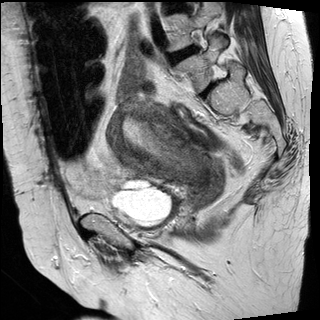
Pelvic MRI for cervical cancer, one sagittal slice; slice 19 of 30 in the series (ordered by position); T2-weighted; 1.5 T; TE 89 ms, TR 3810 ms; 320 × 320 image matrix, field of view 260 × 260 mm. Patient: female, 62 years.
Annotated regions visible in this slice (expert manual segmentation):
- uterus and cervix: bounding box <108,95,226,208> (left, top, right, bottom; pixels)